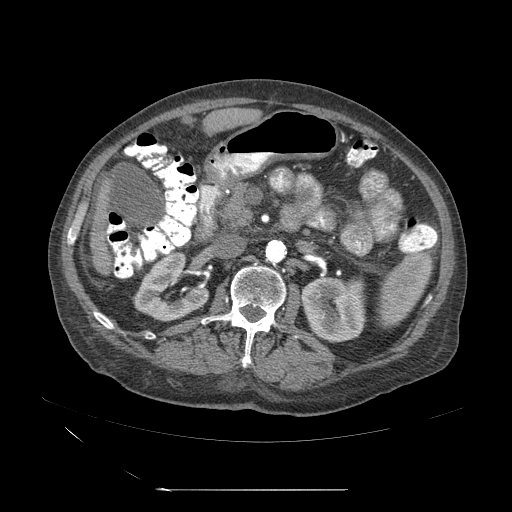
Contrast-enhanced abdominal CT (liver protocol), one axial slice. Position 12 of 71 along the scan axis. Reconstruction kernel STANDARD. 120 kVp. Soft-tissue window (W 400 / L 40 HU). 2.5 mm slice thickness. 512 × 512 image matrix. Case-level facts recorded for this patient, not image findings: diagnosis: hepatocellular carcinoma (patient treated with transarterial chemoembolisation; whether this scan precedes or follows treatment is not stated here); TNM stage (as recorded): Stage-II; Child-Pugh class: A; tumour nodularity: multinodular; tumour size: 1 cm.
Annotated regions visible in this slice (semi-automatic segmentation, software-assisted and operator-edited):
- abdominal aorta: bounding box (x1, y1, x2, y2) in pixels: (265, 241, 286, 264)